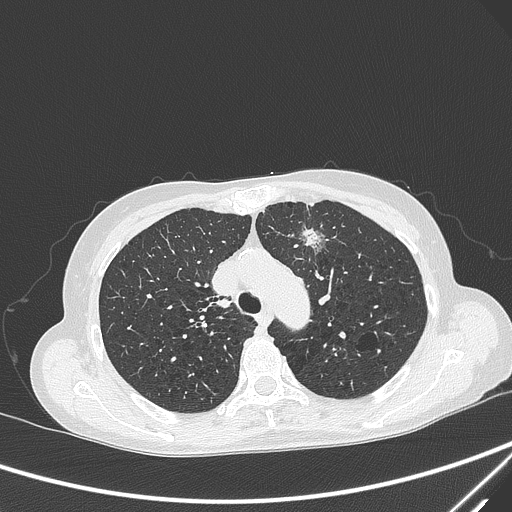
Chest CT, one axial slice. Position 222 of 299 along the scan axis. 120 kVp. Lung window (W 1500 / L -600 HU). 512 × 512 image matrix, field of view 350 × 350 mm. Patient: female, 71 years. Case-level facts recorded for this patient, not image findings: clinical TNM (as recorded): T1c N0 M0; histopathological grade: G2-3.
Outlined on this slice (rectangle marked by the reading radiologist):
- lung tumour (recorded histology: adenocarcinoma): bounding box [x1, y1, x2, y2] px = [297, 218, 325, 261]